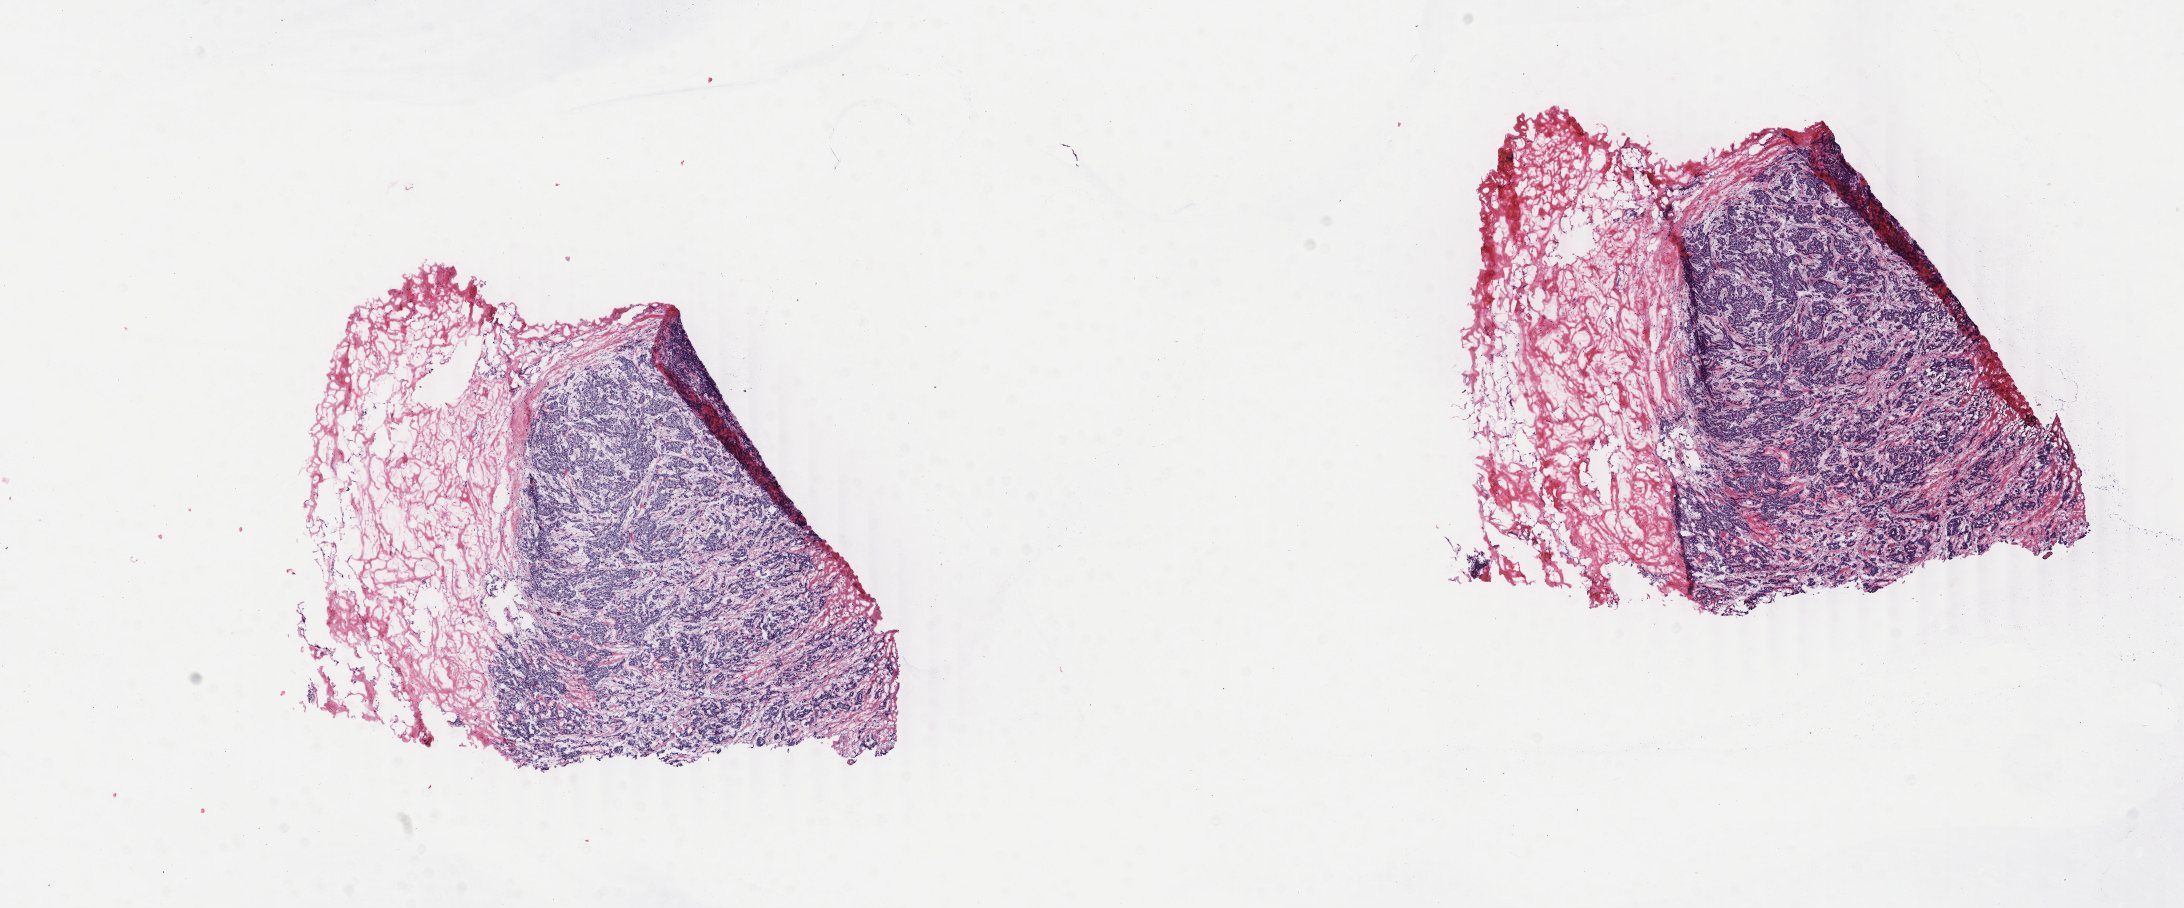
Digitized H&E tissue section (whole slide) — shown as a low-resolution overview of the whole scanned area (about 17.4 x 7.2 mm). Frozen section from the bottom of the tissue portion. Breast, primary tumour sample. Female patient; age at initial diagnosis 43 years. Pathologist review of this section (percent, as recorded): tumour cells 60%, tumour nuclei 70%, normal cells 0%, stromal cells 40%, necrosis 0%. Infiltration values recorded for this section: lymphocyte infiltration 0%, monocyte infiltration 0%, neutrophil infiltration 0%.
Lymph nodes positive (case pathology): 6 of 30 examined. Pathologic diagnosis: Infiltrating duct carcinoma, NOS. Laterality: left.